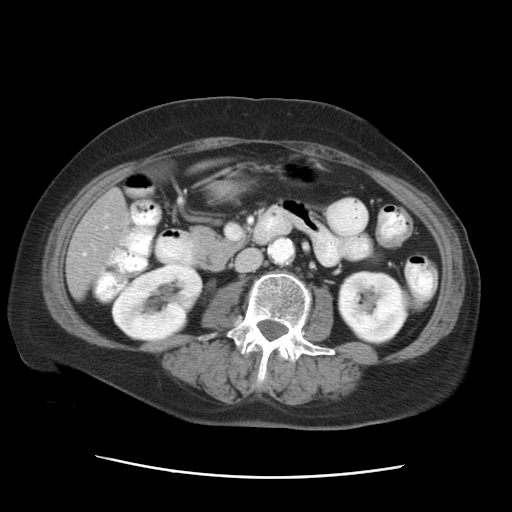
Contrast-enhanced abdominal CT, one axial slice. Position 9 of 29 along the scan axis. 120 kVp. Intravenous contrast given. Soft-tissue window (W 400 / L 40 HU). 7.5 mm slice thickness. 512 × 512 image matrix. Female patient, age 64 years. From the clinical record (not read from this slice): diagnosis: colorectal cancer liver metastases, imaged before liver resection; multiple liver metastases: no; largest metastasis: 2.5 cm; chemotherapy before resection: no.
Annotated regions visible in this slice (outlined manually by an expert reader):
- liver: box from (x=66, y=162) to (x=214, y=297) px
- planned liver remnant (the part of the liver to remain after resection): (x=66, y=162)–(x=214, y=296)
- portal vein (with intrahepatic branches): (x=226, y=226)–(x=237, y=240)